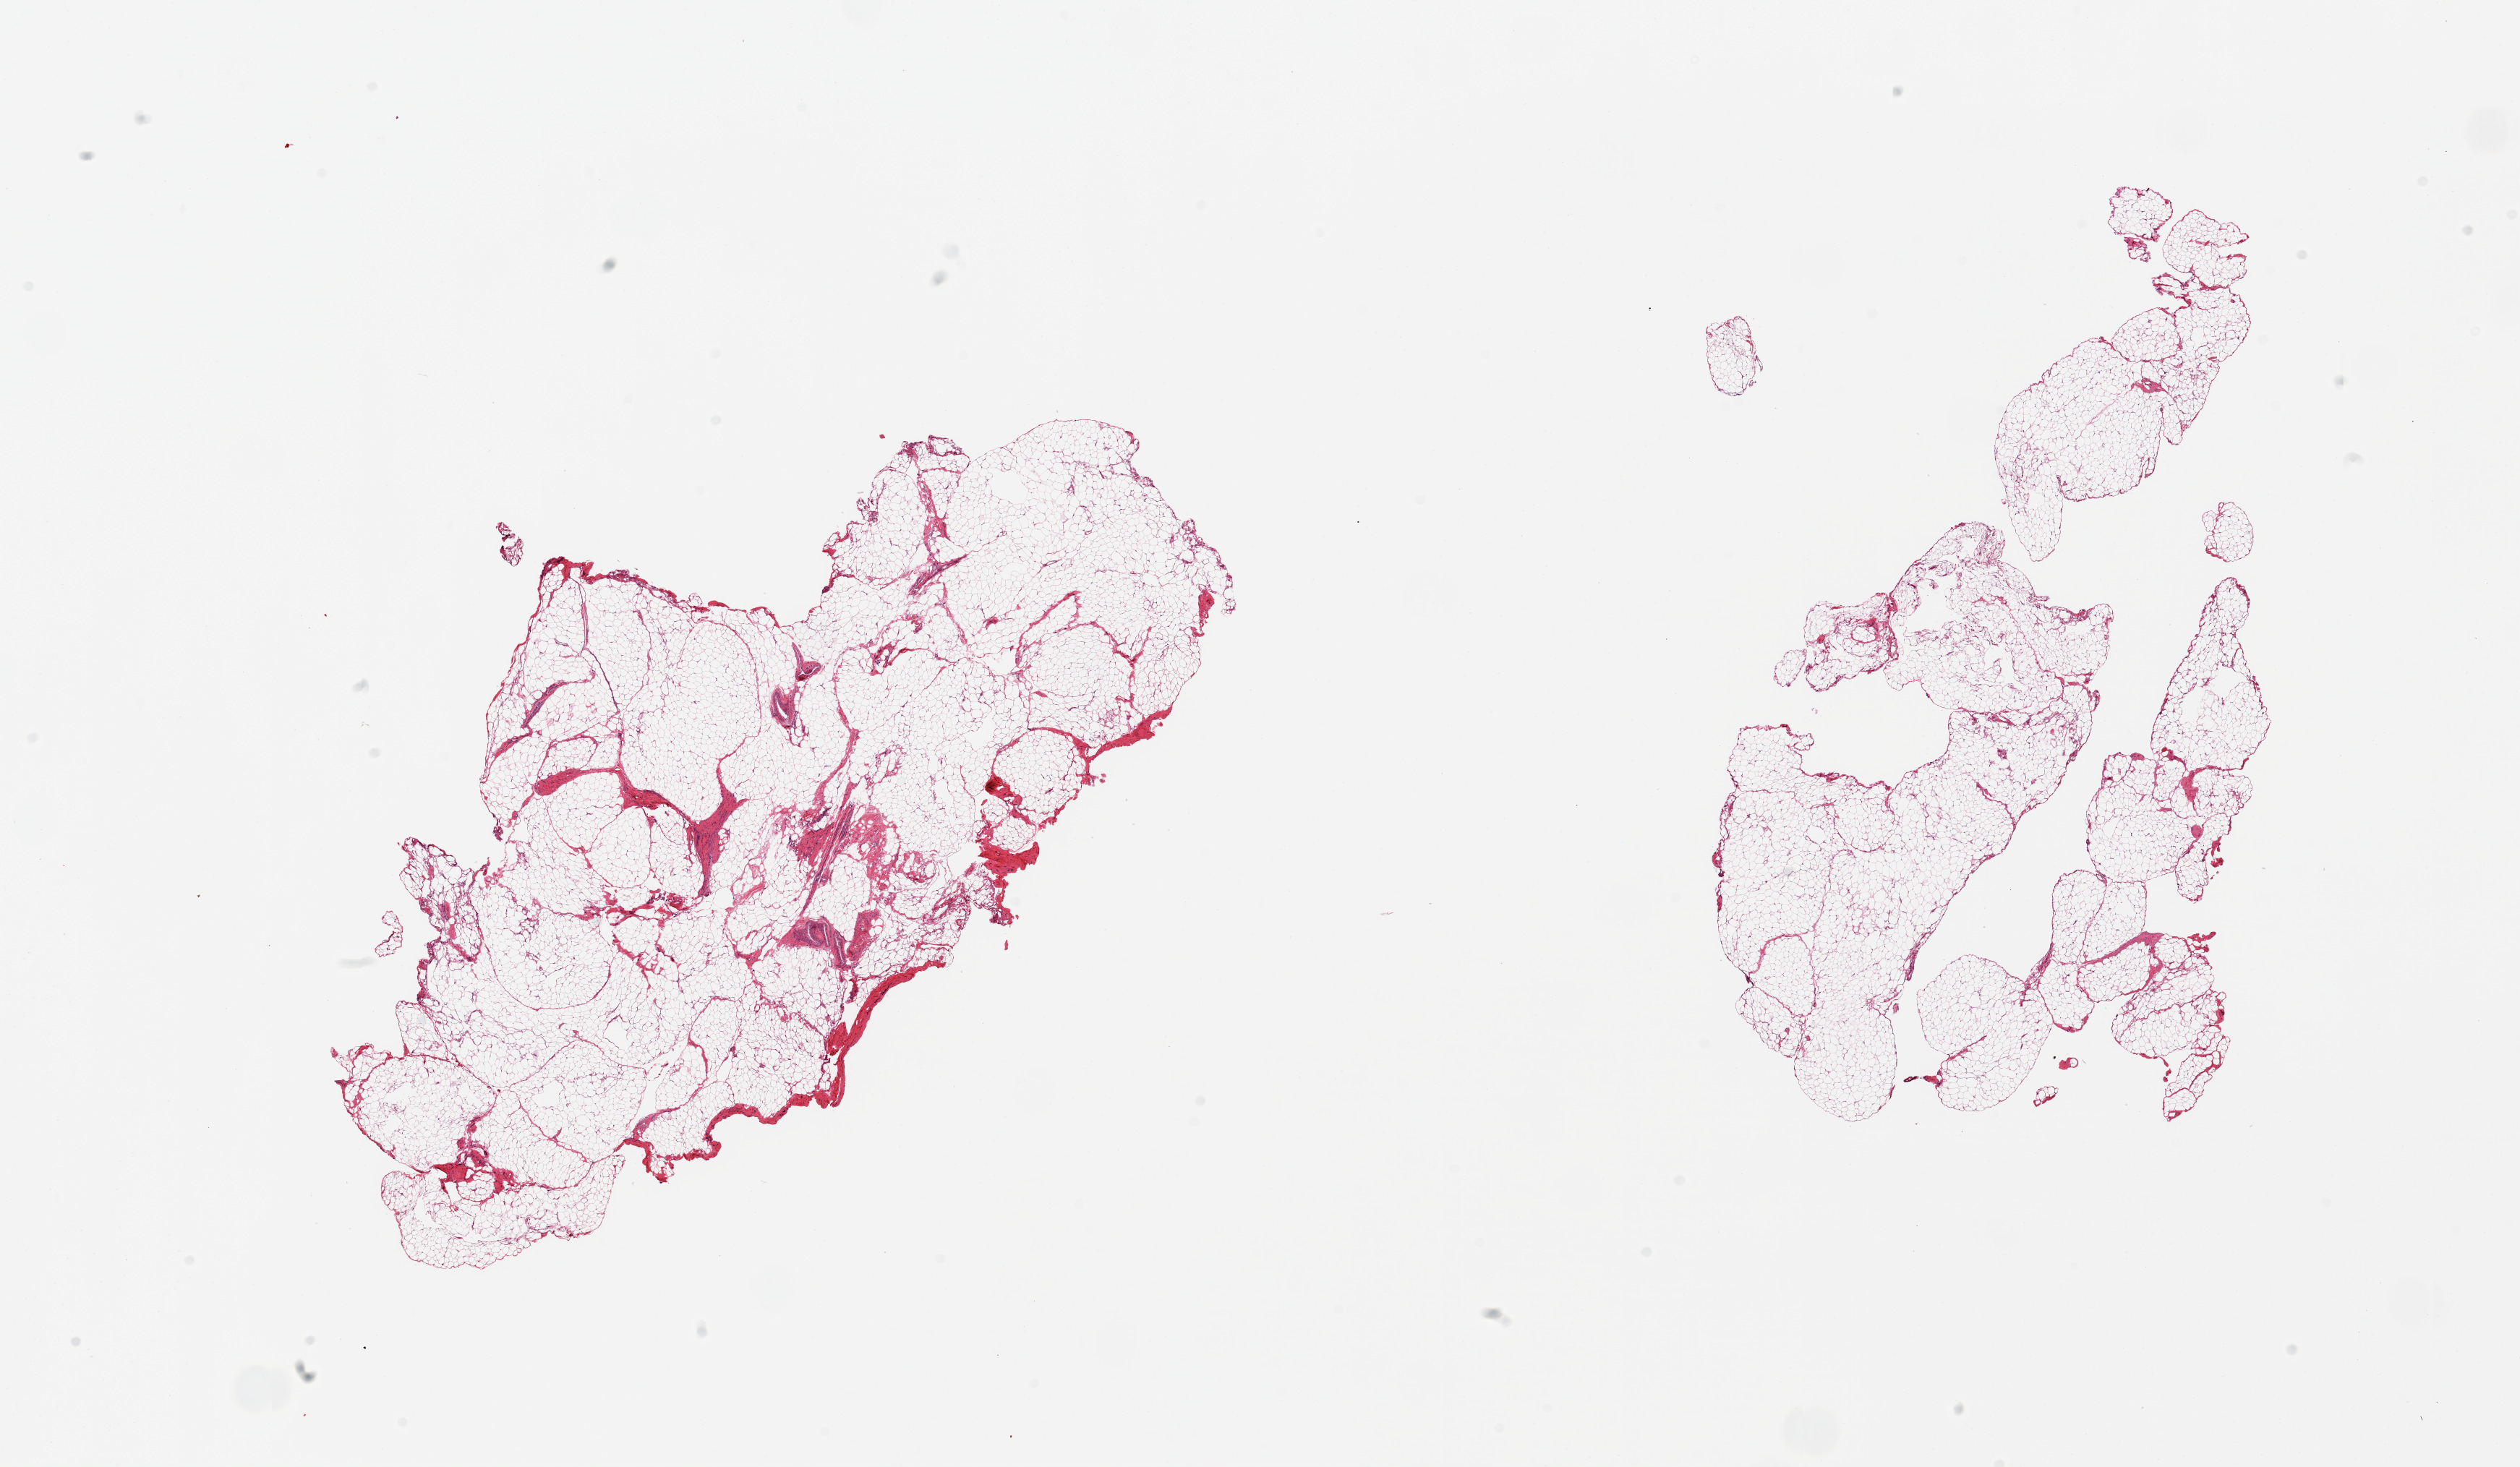
Digitized haematoxylin and eosin-stained section, whole scanned area (about 27.6 x 16.0 mm) shown as a low-resolution overview, PAXgene-fixed paraffin-embedded (PFPE) section, section of omentum (target tissue), donor tissue sample. Female donor.
Pathologist's review note for this sample: 2 pieces.